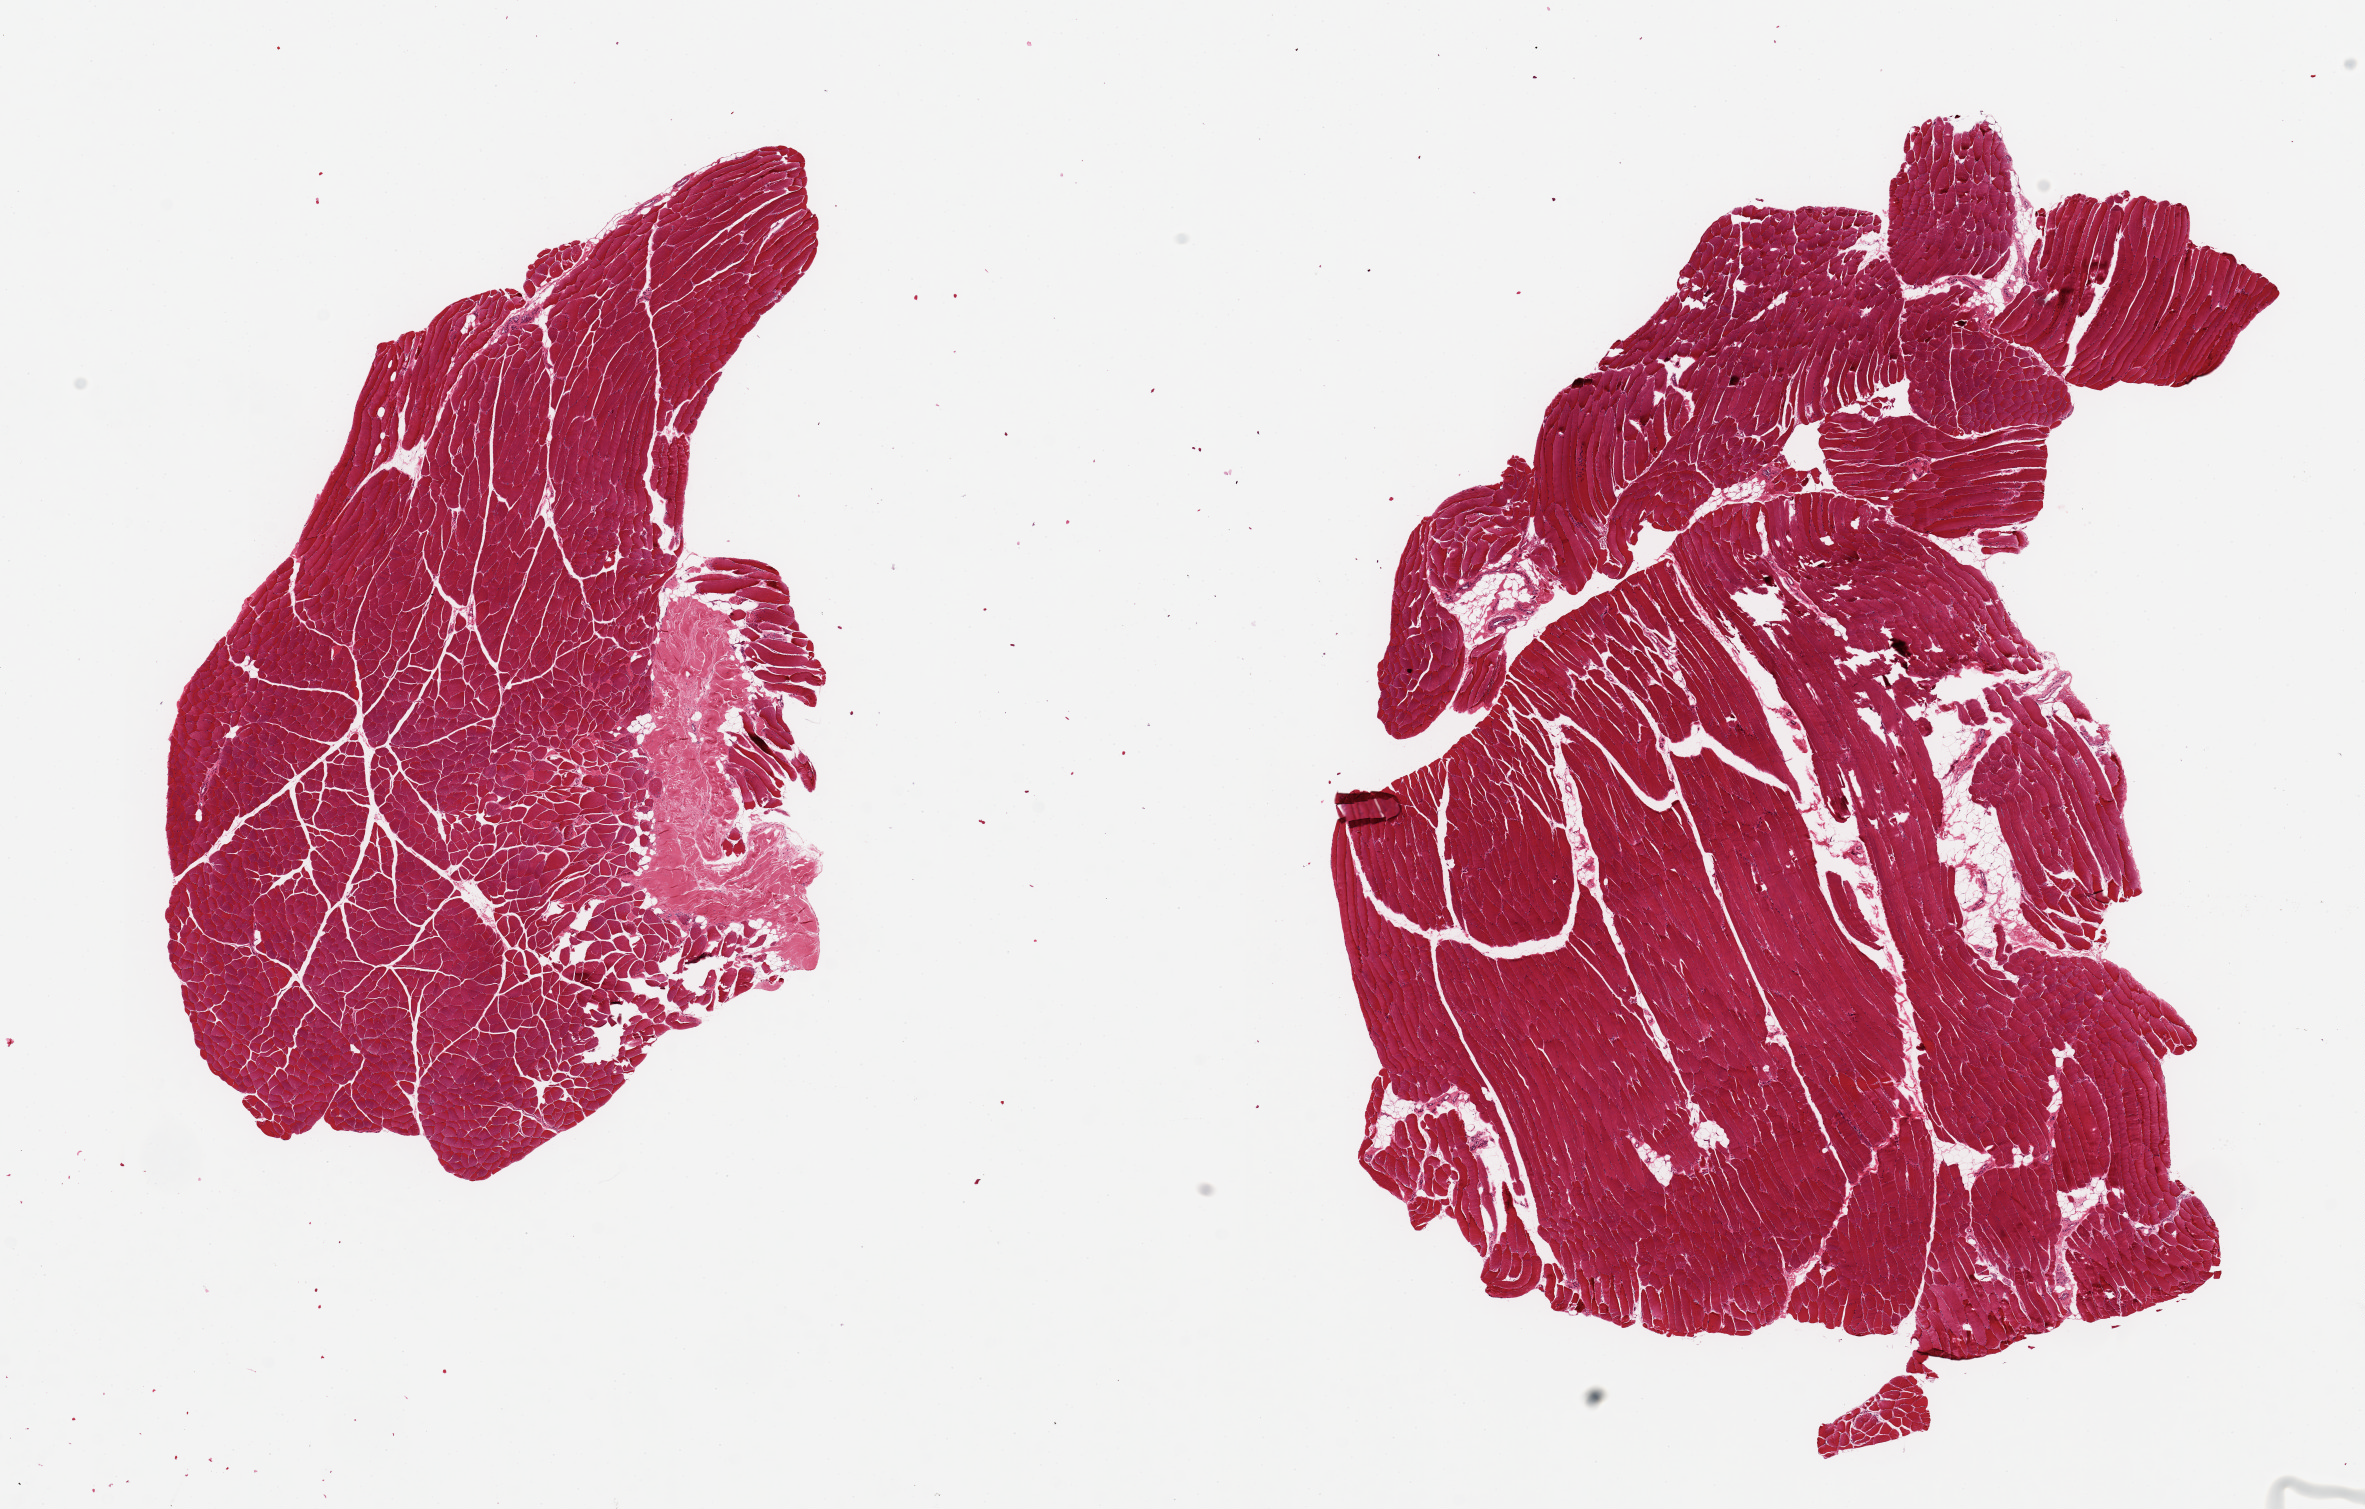
Digitized hematoxylin and eosin (H&E)-stained section, brightfield, low-resolution overview of the scanned area, about 18.7 x 11.9 mm (acquisition: 20x scan). PAXgene-fixed paraffin-embedded (PFPE) section. Target tissue: skeletal muscle. Tissue donor sample.
Review note (as recorded): 2 aliquots, ~ 8x5mm; Minimal interstitial fat.